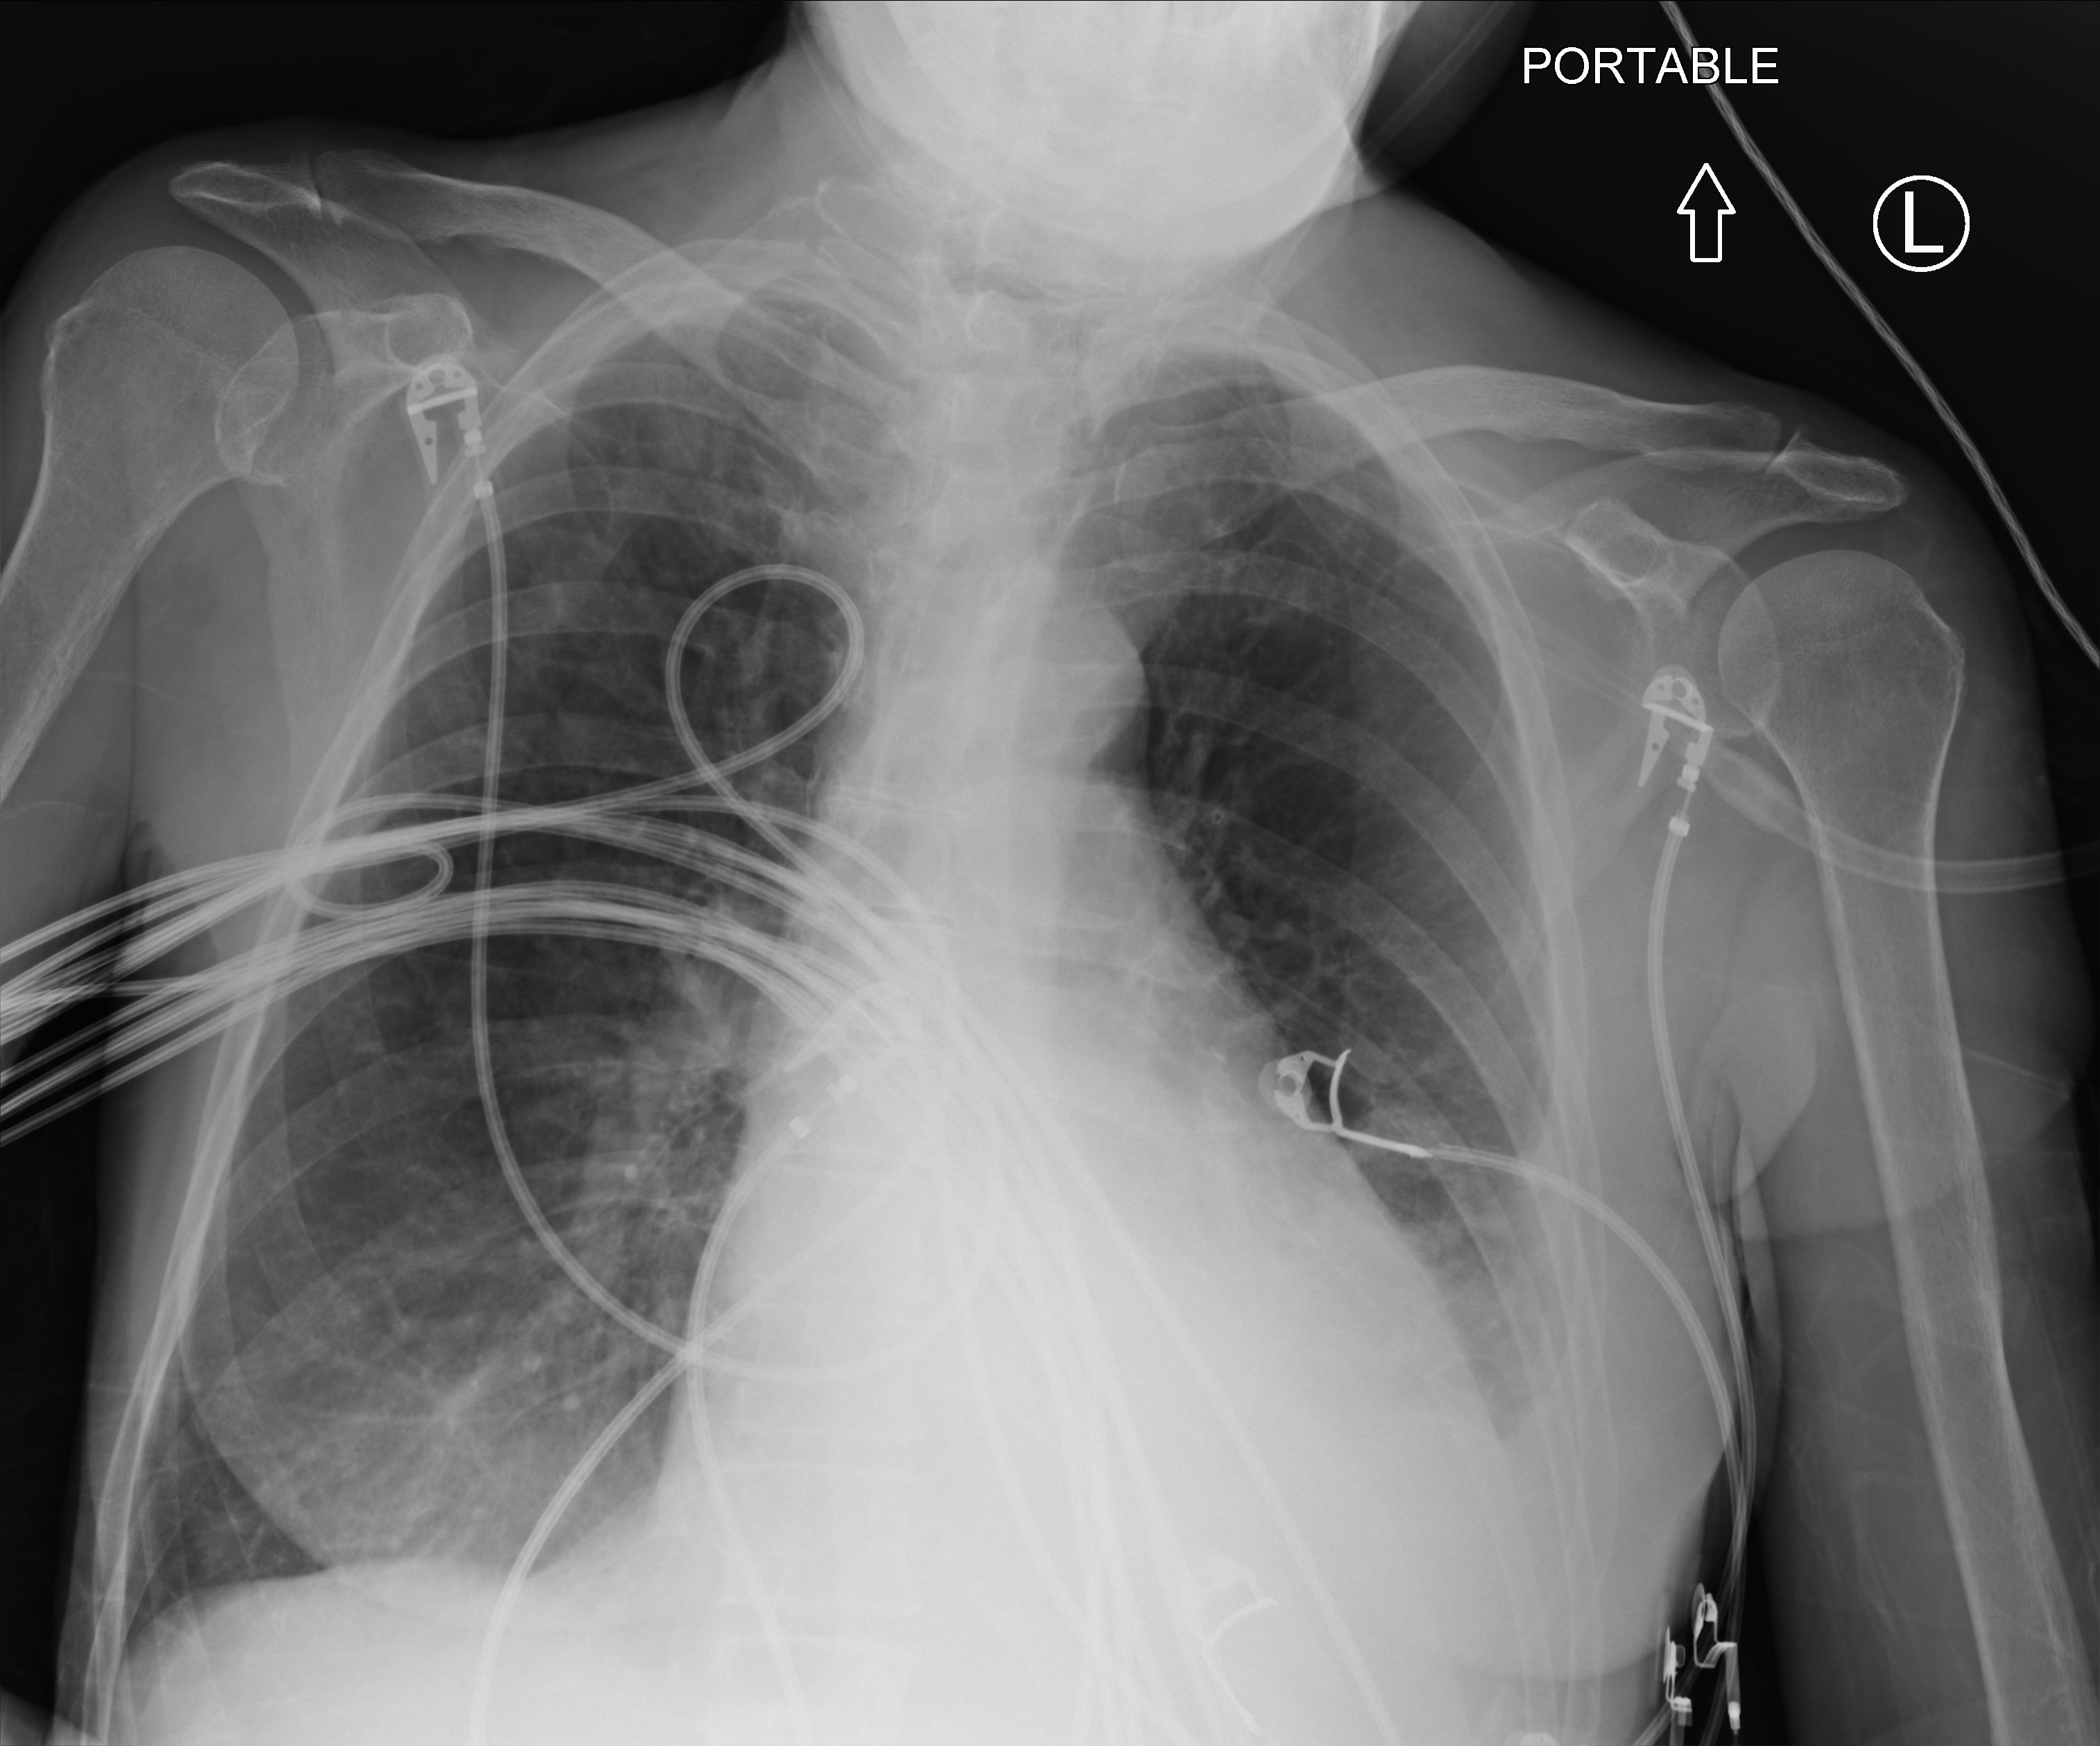
Chest X-ray (portable); anteroposterior (AP) projection. Patient hospitalised with COVID-19; female, aged 60–74 years.
Hospital-stay facts (about this admission, not read from this image; timing relative to this image not recorded): admitted to intensive care during this hospital stay: yes; mechanically ventilated during this hospital stay: yes.